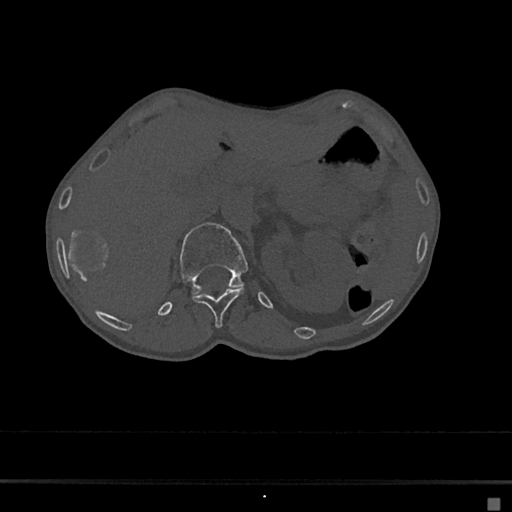
CT including the spine, one axial slice; slice 96 of 797 in the series (ordered by position); bone window (W 1800 / L 400 HU); 0.5 mm slice thickness; 512 × 512 image matrix, field of view 360 × 360 mm. Female patient, age 68 years. Case-level facts recorded for this patient, not image findings: primary cancer: renal.
Outlined on this slice (semi-automatic segmentation, software-assisted and operator-edited):
- L1 vertebra: bounding box <180,223,249,295> (left, top, right, bottom; pixels)
- T12 vertebra: <193,288,244,329>